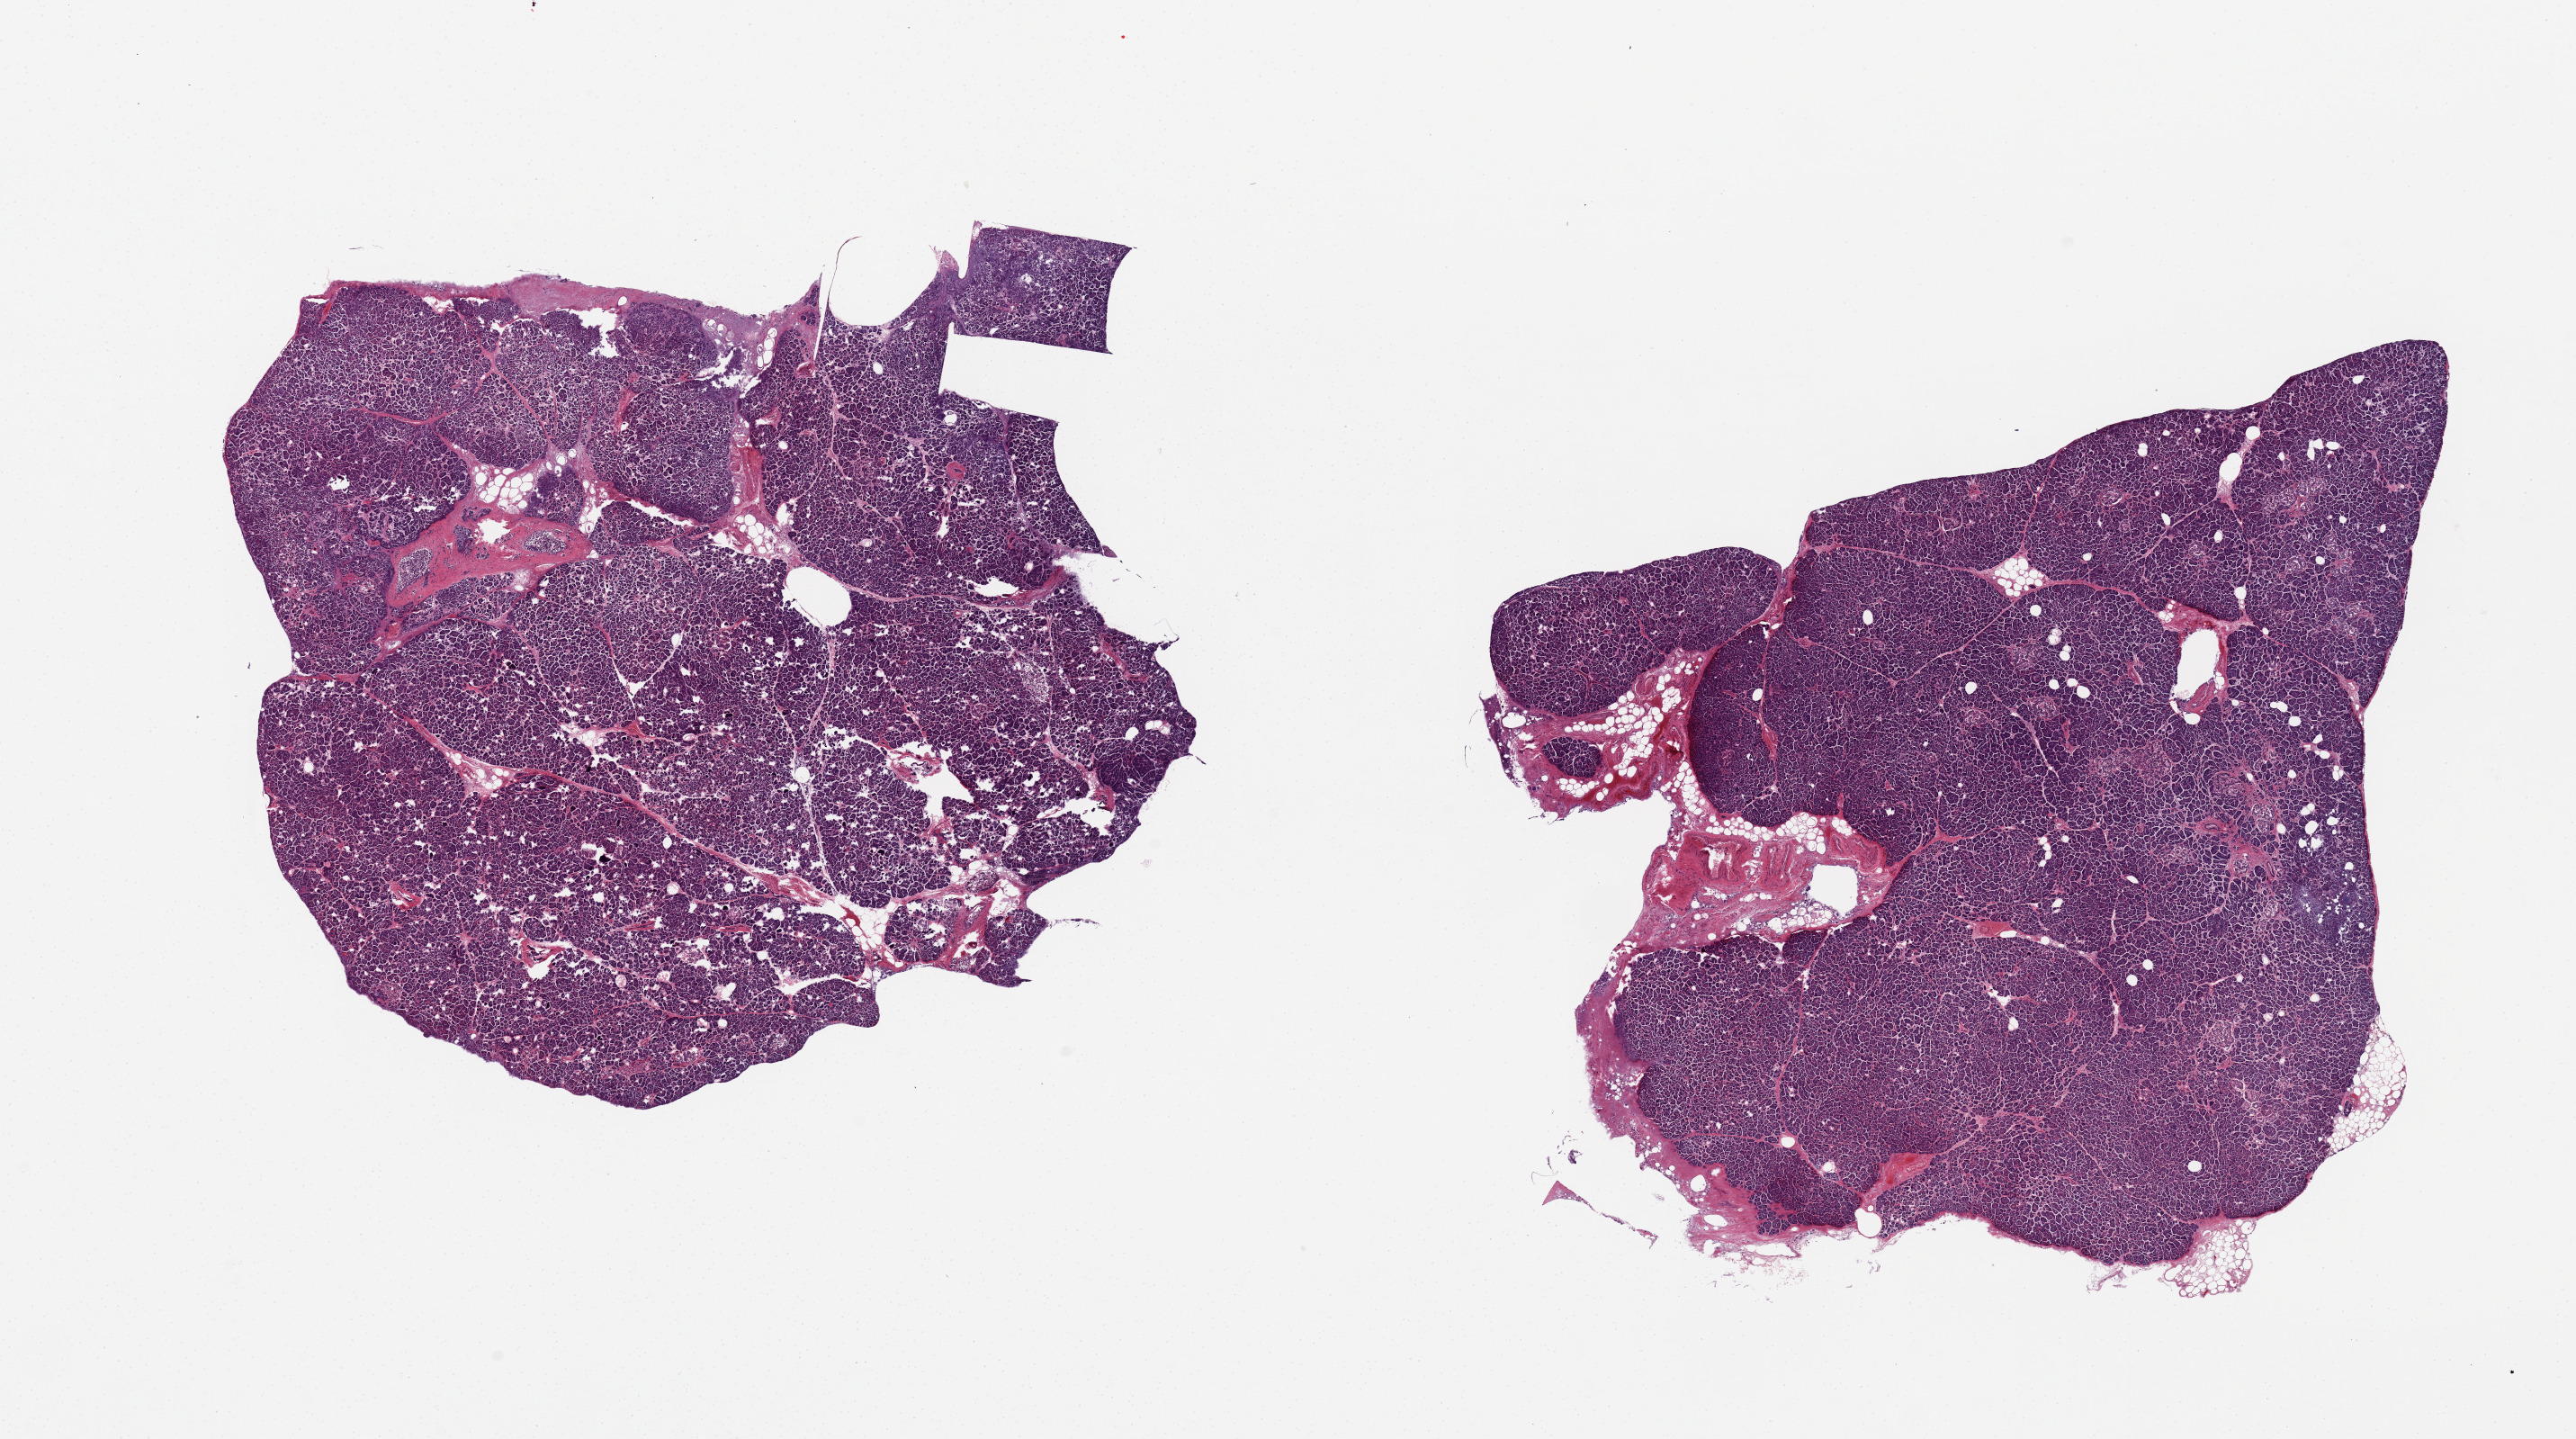
Whole-slide image, hematoxylin and eosin (H&E) stain — low-resolution overview of the scanned area, about 22.6 x 12.6 mm (from a 20x scan), PAXgene-fixed, paraffin-embedded tissue, section of pancreas (target tissue), tissue donor sample. Female donor.
* review note (as recorded): 2 pieces, moderate-severe saponification/autolysis; Rare islets visible